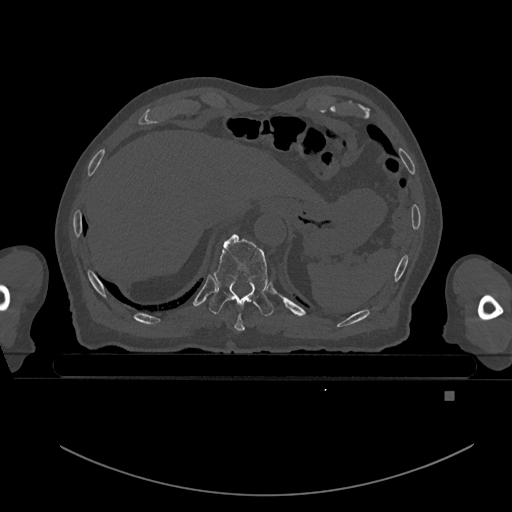
CT including the spine, one axial slice. Slice 98 of 969 in the series (ordered by position). Bone window (W 1800 / L 400 HU). 0.5 mm slice thickness. 512 × 512 image matrix, field of view 456 × 456 mm. Patient: male, 82 years. Case-level facts recorded for this patient, not image findings: primary cancer: prostate.
Outlined on this slice (semi-automatic segmentation, software-assisted and operator-edited):
- T10 vertebra: bounding box (x1, y1, x2, y2) in pixels: (209, 233, 274, 317)
- T9 vertebra: (234, 314, 245, 332)